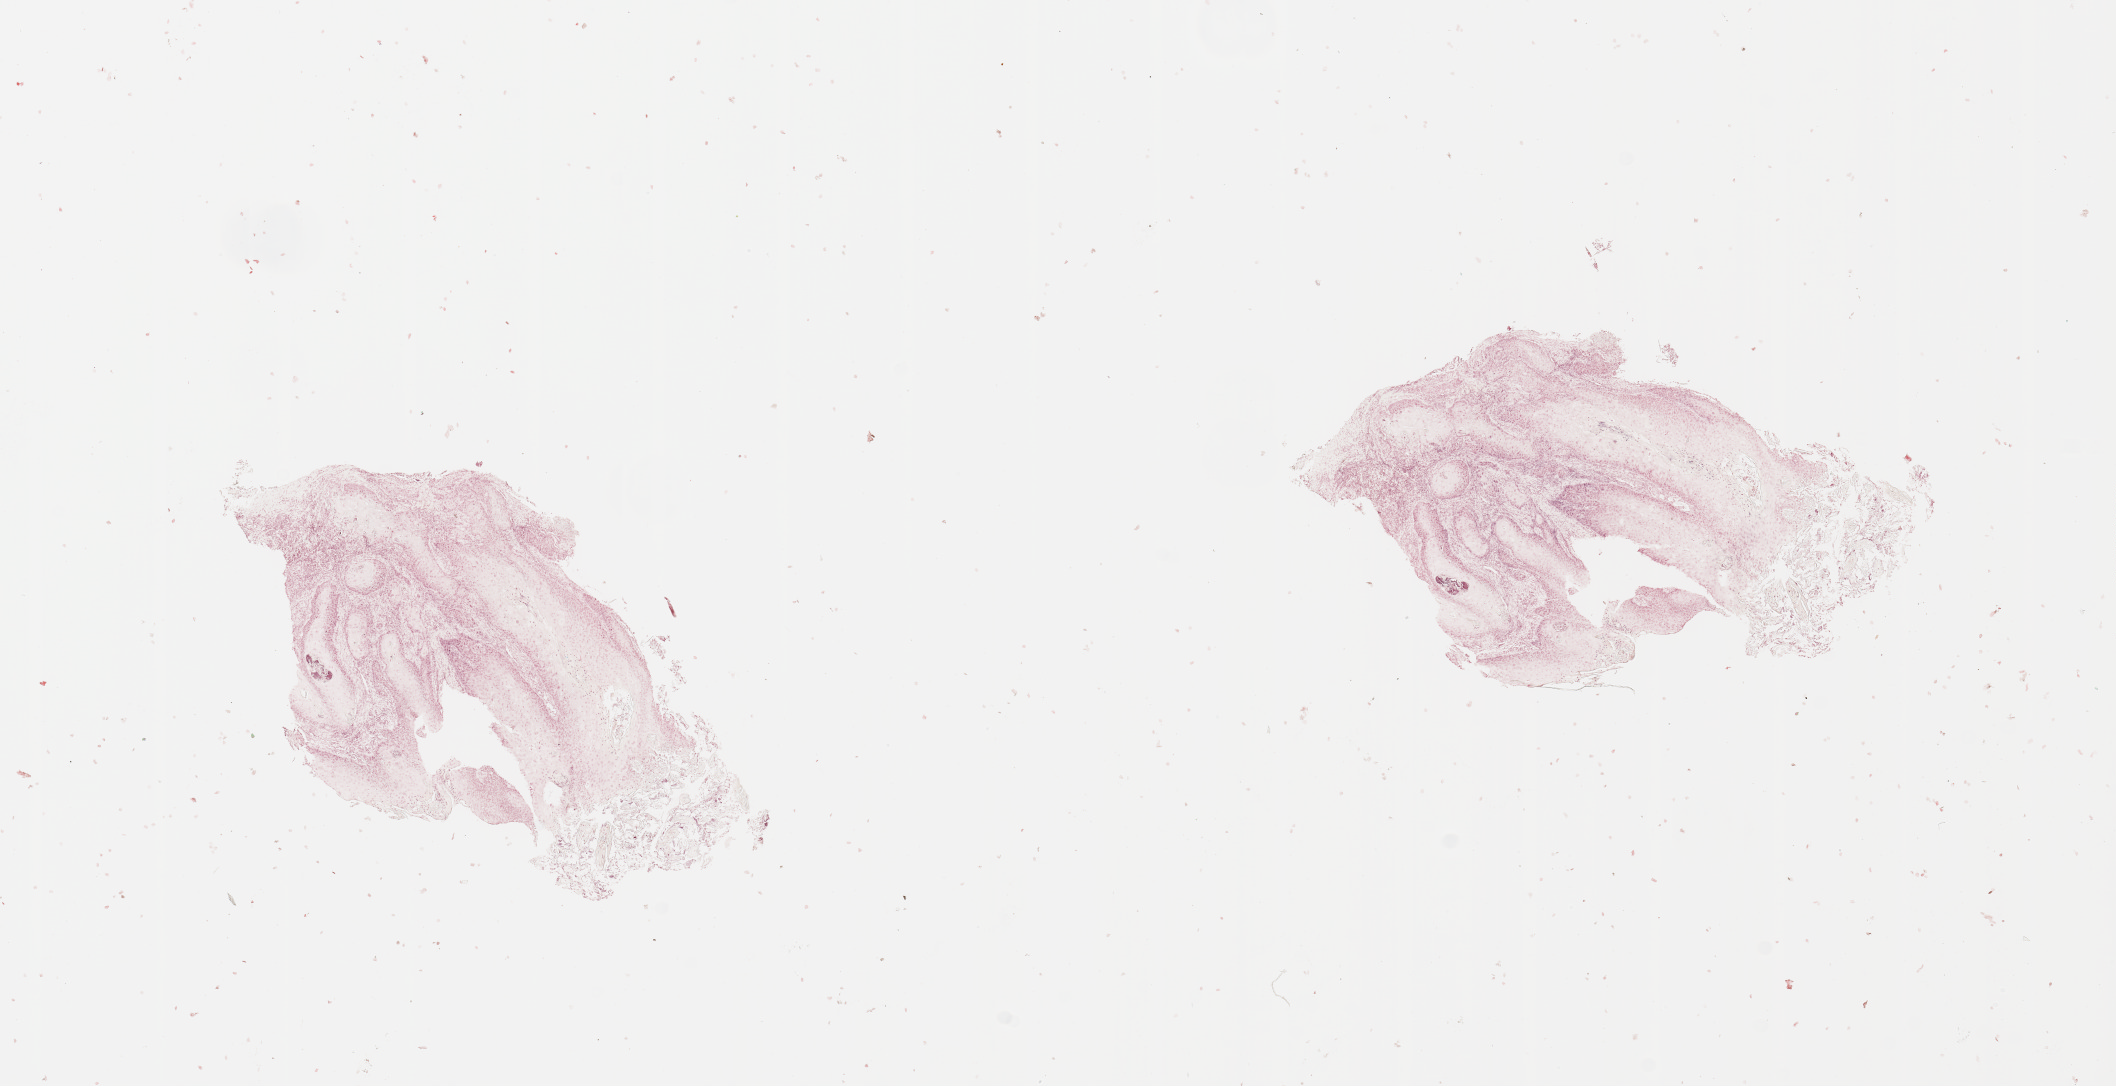
Whole-slide histology image, H&E-stained — low-resolution overview of the scanned area, about 16.7 x 8.6 mm. Tumour tissue sample, sampled site: larynx. Male, 64 y/o. Histologic grade: G2 (moderately differentiated). Composition of this section per pathologist review: tumour nuclei 85%, necrosis 10%.
Diagnosis: Squamous cell carcinoma, NOS (larynx, NOS). AJCC pathologic stage: II. Primary tumour site (as recorded): larynx.